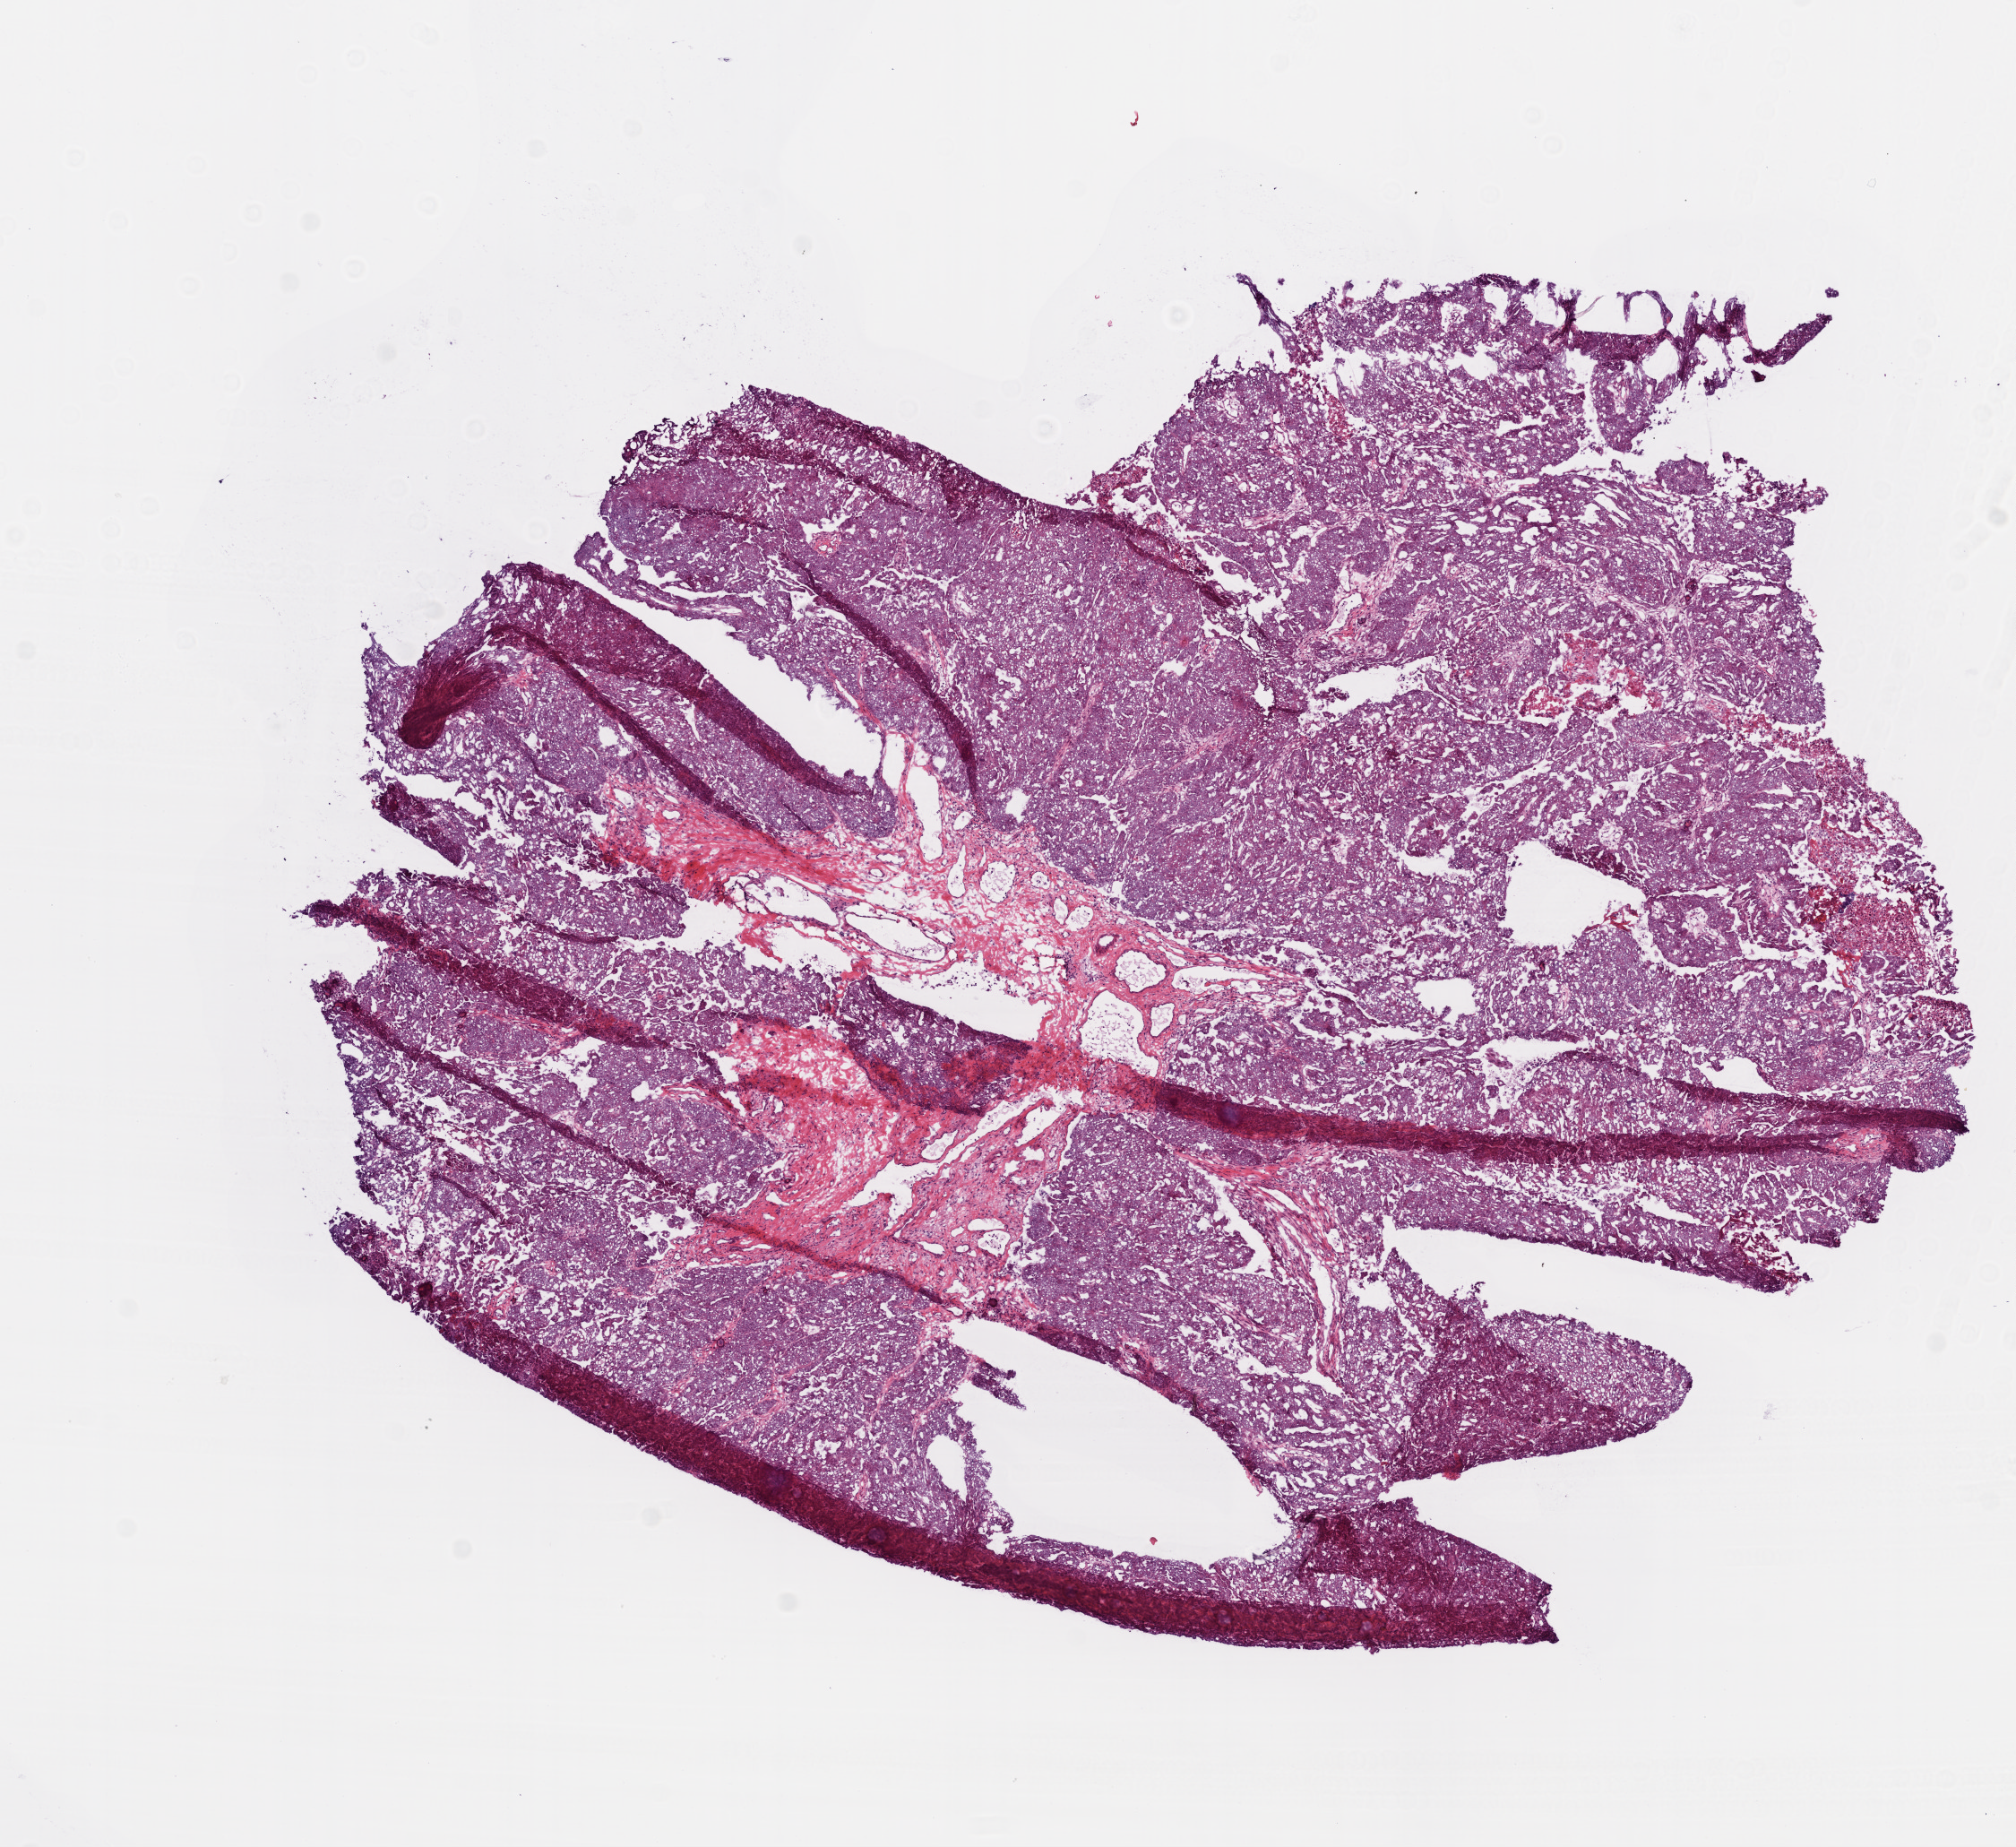
Digitized H&E tissue section (whole slide) — a low-resolution overview of the entire scanned area, about 9.0 x 8.3 mm; frozen section from the bottom of the tissue portion; primary tumour sample from the ovary. Patient: female, age at initial diagnosis 85 years. Histologic grade: G3 (poorly differentiated). Pathologist review of this section (percent, as recorded): tumour cells 85%, tumour nuclei 95%, normal cells 0%, stromal cells 10%, necrosis 5%.
Diagnosis: Serous cystadenocarcinoma, NOS. FIGO stage: IIIC.